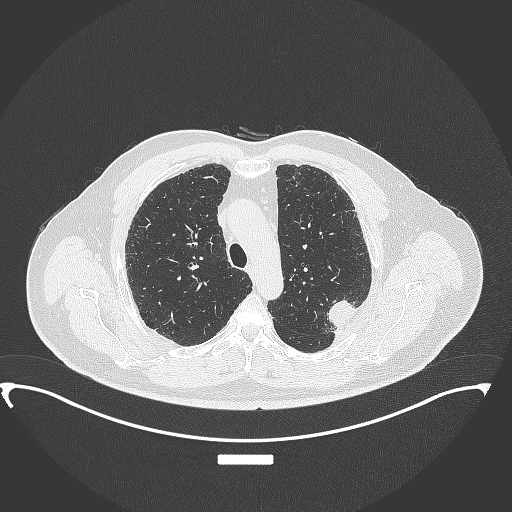
Chest CT, one axial slice; slice 268 of 350 in the series (ordered by position); reconstruction kernel B70f; 120 kVp; lung window (W 1500 / L -600 HU); 1 mm slice thickness; 512 × 512 image matrix, field of view 459 × 459 mm. Male patient, age 64 years. From the clinical record (not read from this slice): clinical TNM (as recorded): T1c N1 M1.
Annotated regions visible in this slice (bounding box drawn by a radiologist):
- lung tumour (recorded histology: adenocarcinoma): bounding box [x1, y1, x2, y2] px = [322, 293, 363, 333]